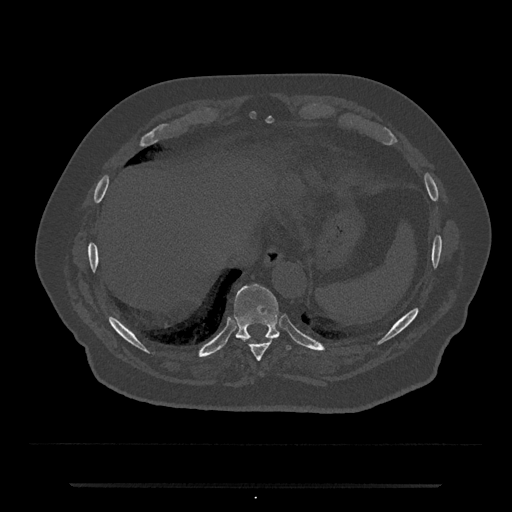
CT including the spine, one axial slice; 120 kVp; bone window (W 1800 / L 400 HU); 512 × 512 image matrix. Patient: male, 80 years. From the clinical record (not read from this slice): primary cancer: prostate.
Annotated regions visible in this slice (semi-automatically segmented with operator editing):
- T10 vertebra: bounding box (x1, y1, x2, y2) in pixels: (234, 284, 291, 349)
- T9 vertebra: (242, 338, 275, 361)